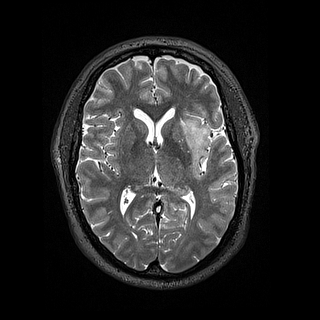
Brain MRI from a brain-tumour surgery series, one axial slice; slice 82 of 144 in the series (ordered by position); 320 × 320 image matrix. Case-level facts recorded for this patient, not image findings: histopathology: Astrocytoma; WHO grade: 2; IDH mutation: yes.
Structures marked on this image (expert manual segmentation):
- tumour: box from (x=181, y=112) to (x=211, y=178) px